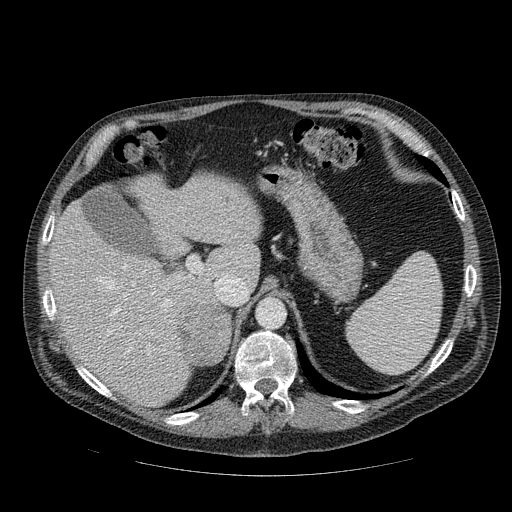
Contrast-enhanced abdominal CT, one axial slice. Slice 68 of 111 in the series (ordered by position). Reconstruction kernel STANDARD. Soft-tissue window (W 400 / L 40 HU). 2.5 mm slice thickness. 512 × 512 image matrix, field of view 420 × 420 mm. Patient: male, 56 years. Case-level facts recorded for this patient, not image findings: diagnosis: adrenocortical carcinoma; tumour side: right adrenal; tumour size at pathology: 9 cm; Ki-67 index: 48 %; stage (as recorded): 4.
Structures marked on this image (semi-automatically segmented with operator editing):
- mass: bounding box <181,302,231,364> (left, top, right, bottom; pixels)